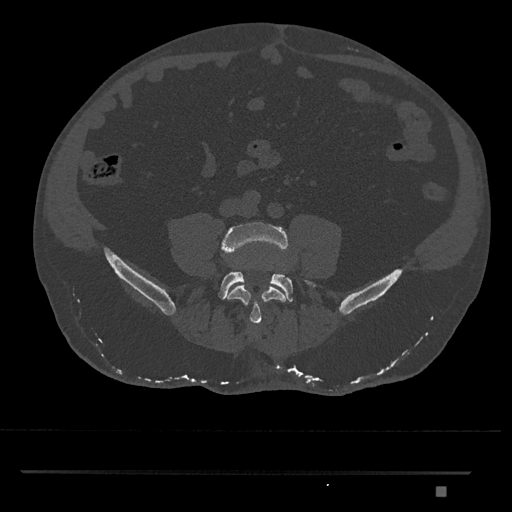
CT including the spine, one axial slice. Slice 584 of 1134 in the series (ordered by position). Reconstruction kernel Br40s/3. 120 kVp. Bone window (W 1800 / L 400 HU). 0.5 mm slice thickness. 512 × 512 image matrix, field of view 429 × 429 mm. Male patient, age 65 years. From the clinical record (not read from this slice): primary cancer: prostate.
Annotated regions visible in this slice (semi-automatic segmentation, software-assisted and operator-edited):
- L4 vertebra: box from (x=221, y=222) to (x=291, y=325) px
- L5 vertebra: (x=218, y=269)–(x=316, y=302)